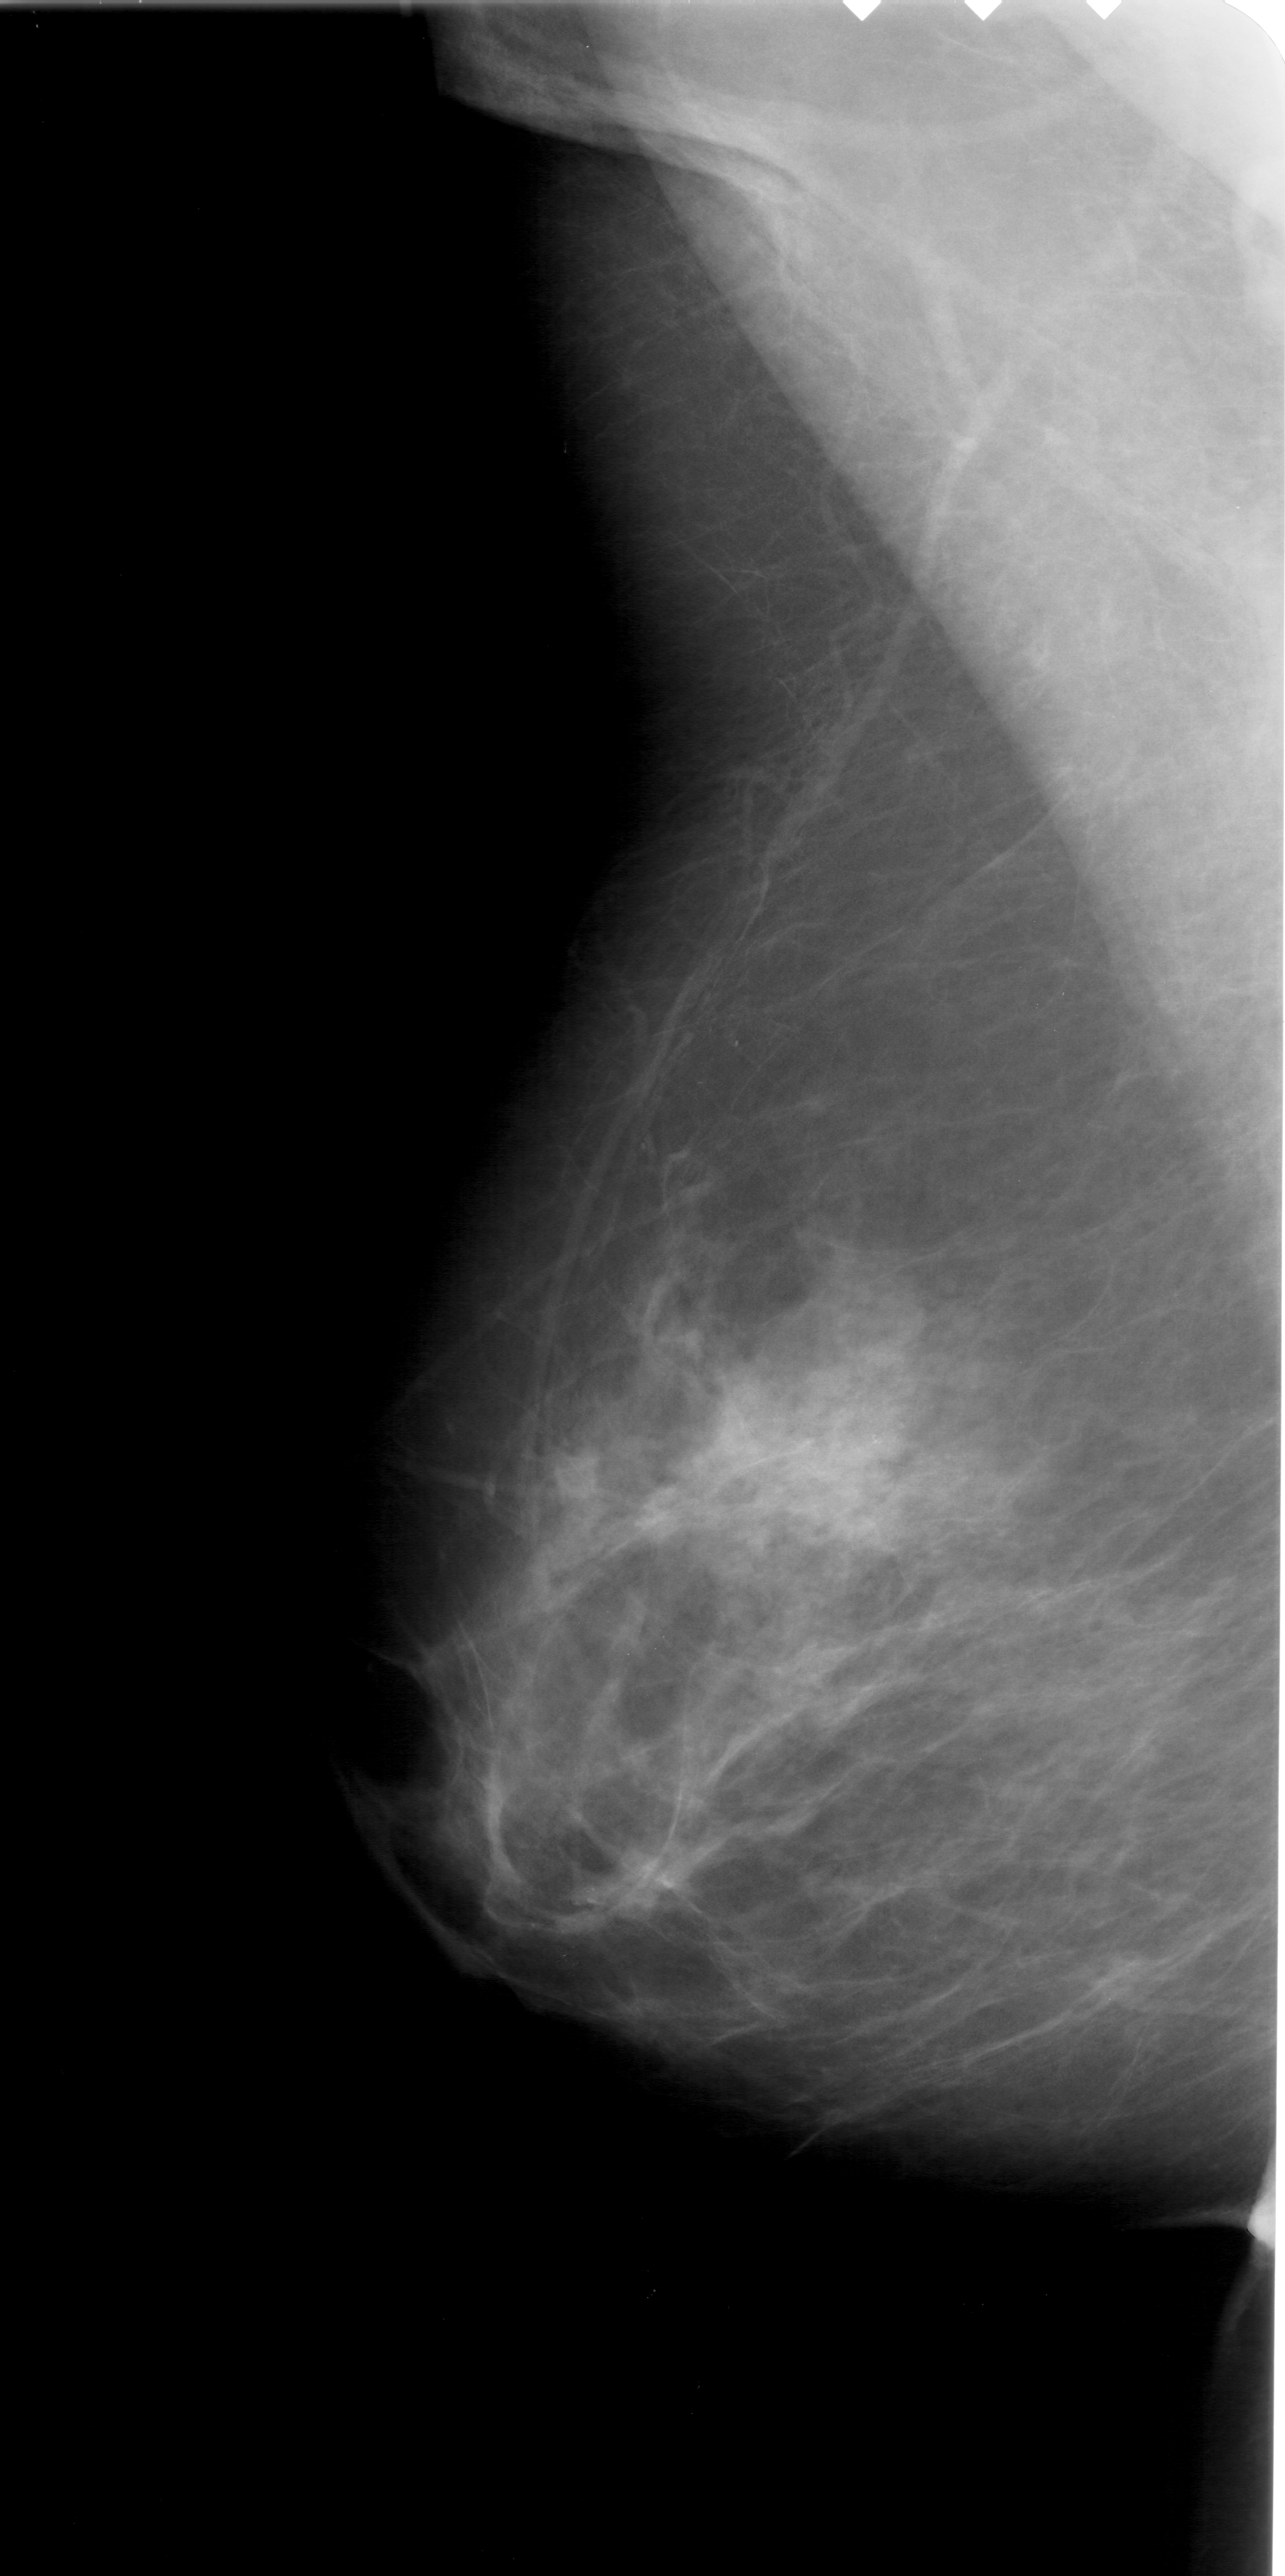
Mammogram (digitized film); left breast; mediolateral oblique (MLO) view; BI-RADS breast density category 3 (scale 1–4).
- Calcifications, morphology pleomorphic, distribution clustered; BI-RADS assessment category 4; pathology result (as recorded, not read from the image): malignant.